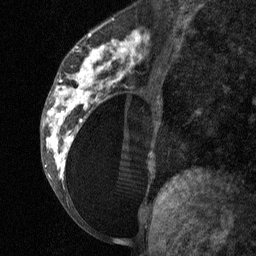
Breast MRI (dynamic contrast-enhanced), one sagittal slice. Slice 31 of 64 in the series (ordered by position). Dynamic contrast-enhanced study with each time point stored as its own series, time point 2 of 3 at this slice position (early post-contrast, ordered by acquisition time). 1.5 T. TE 4.8 ms, TR 27 ms. 2 mm slice thickness. 256 × 256 image matrix, field of view 180 × 180 mm. Patient: female, 34 years. From the clinical record (not read from this slice): setting: breast cancer imaged before/during neoadjuvant chemotherapy; receptor status: HR-positive, HER2-negative.
Annotated regions visible in this slice (semi-automatically segmented with operator editing):
- analysis volume of interest (the breast-tissue region the enhancement analysis was run in; not a lesion): bounding box (x1, y1, x2, y2) in pixels: (41, 23, 157, 197)
- tumour enhancement mask (voxels above the 90 % enhancement threshold inside the analysis volume of interest): (46, 31, 142, 179)